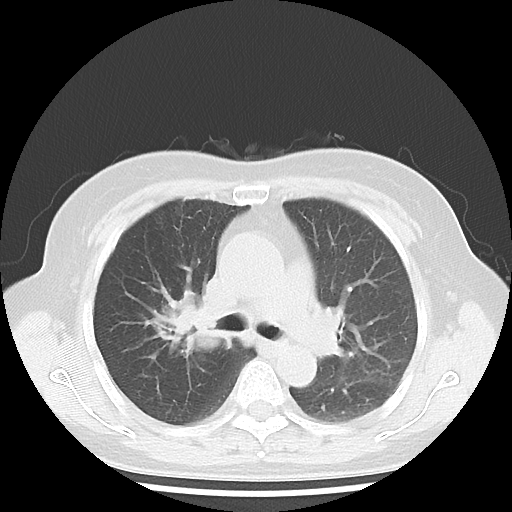
Chest CT, one axial slice. Slice 26 of 43 in the series (ordered by position). Reconstruction kernel LUNG. Lung window (W 1500 / L -600 HU). 5 mm slice thickness. 512 × 512 image matrix, field of view 316 × 316 mm. Patient: female, 62 years. Case-level facts recorded for this patient, not image findings: clinical TNM (as recorded): T3 N0 M0.
Annotated regions visible in this slice (bounding box drawn by a radiologist):
- lung tumour (recorded histology: small cell carcinoma): bounding box <144,273,232,370> (left, top, right, bottom; pixels)